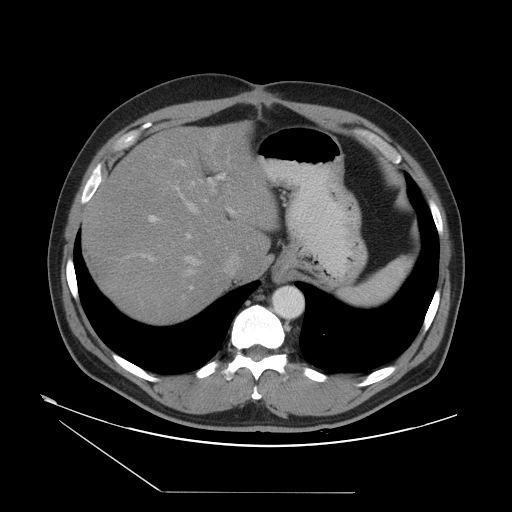
Contrast-enhanced abdominal CT, one axial slice. Slice 39 of 55 in the series (ordered by position). Intravenous contrast given. Soft-tissue window (W 400 / L 40 HU). 5 mm slice thickness. 512 × 512 image matrix, field of view 454 × 454 mm. Male patient, age 59 years. From the clinical record (not read from this slice): diagnosis: colorectal cancer liver metastases, imaged before liver resection; multiple liver metastases: yes; largest metastasis: 0.3 cm; disease in both lobes: yes.
Annotated regions visible in this slice (expert manual segmentation):
- hepatic veins: bounding box [x1, y1, x2, y2] px = [182, 181, 255, 299]
- liver: [86, 125, 275, 320]
- planned liver remnant (the part of the liver to remain after resection): [86, 149, 267, 320]
- portal vein (with intrahepatic branches): [126, 160, 225, 290]
- liver metastasis: [95, 259, 101, 267]